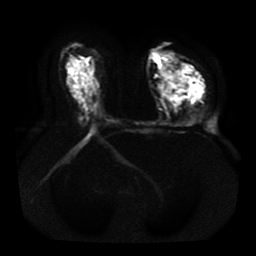
Breast MRI, one axial slice; diffusion-weighted series; image 2 of 4 stored at this slice position (different b-values; order by instance number); 1.5 T; 256 × 256 image matrix, field of view 330 × 330 mm. Female patient.
Structures marked on this image (outlined manually by an expert reader):
- tumour on diffusion-weighted imaging: box from (x=161, y=73) to (x=204, y=99) px